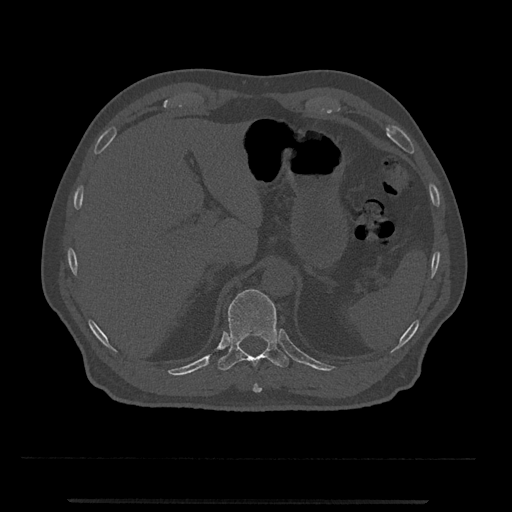
CT including the spine, one axial slice. Position 473 of 797 along the scan axis. 120 kVp. Bone window (W 1800 / L 400 HU). 0.5 mm slice thickness. 512 × 512 image matrix, field of view 419 × 419 mm. Male patient, age 63 years. From the clinical record (not read from this slice): primary cancer: prostate.
Annotated regions visible in this slice (semi-automatic segmentation, software-assisted and operator-edited):
- T10 vertebra: bounding box (x1, y1, x2, y2) in pixels: (253, 383, 262, 393)
- T11 vertebra: (218, 289, 289, 371)